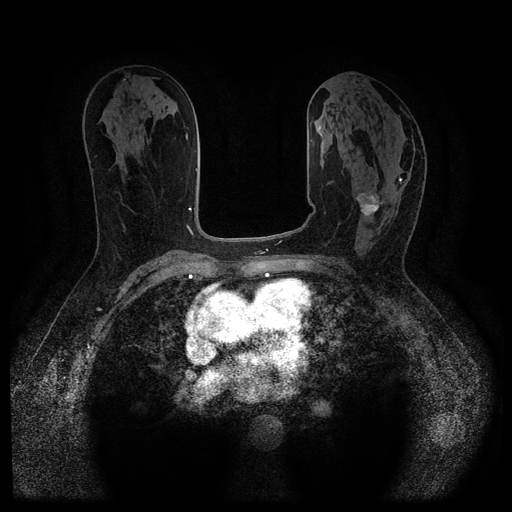
Breast MRI (dynamic contrast-enhanced, multi-phase), one axial slice. Slice 55 of 116 in the series (ordered by position). Dynamic contrast-enhanced series, time point 2 of 5 at this slice position (early post-contrast). 1.5 T. TE 2.6 ms, TR 5.4 ms. 2 mm slice thickness. 512 × 512 image matrix, field of view 340 × 340 mm. Female patient, age 64 years.
Outlined on this slice (semi-automatic segmentation, software-assisted and operator-edited):
- breast lesion (labelled 'tumour' in the annotation; benign lesions carry a separate 'benign' label): box from (x=356, y=193) to (x=385, y=216) px